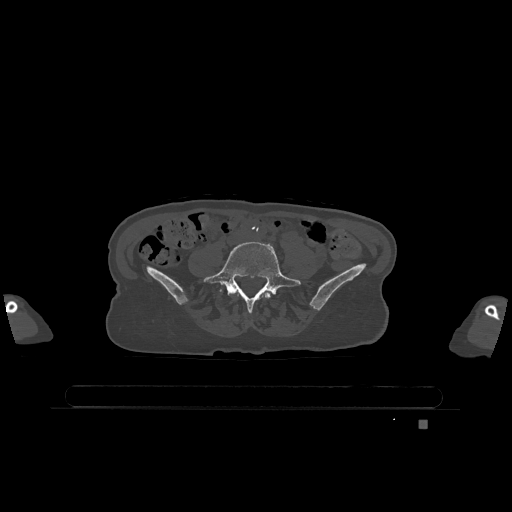
CT including the spine, one axial slice. Position 248 of 1317 along the scan axis. Bone window (W 1800 / L 400 HU). 0.5 mm slice thickness. 512 × 512 image matrix. Female patient, age 74 years. From the clinical record (not read from this slice): primary cancer: lung.
Outlined on this slice (semi-automatically segmented with operator editing):
- L4 vertebra: box from (x=264, y=292) to (x=271, y=298) px
- L5 vertebra: (x=204, y=241)–(x=301, y=312)